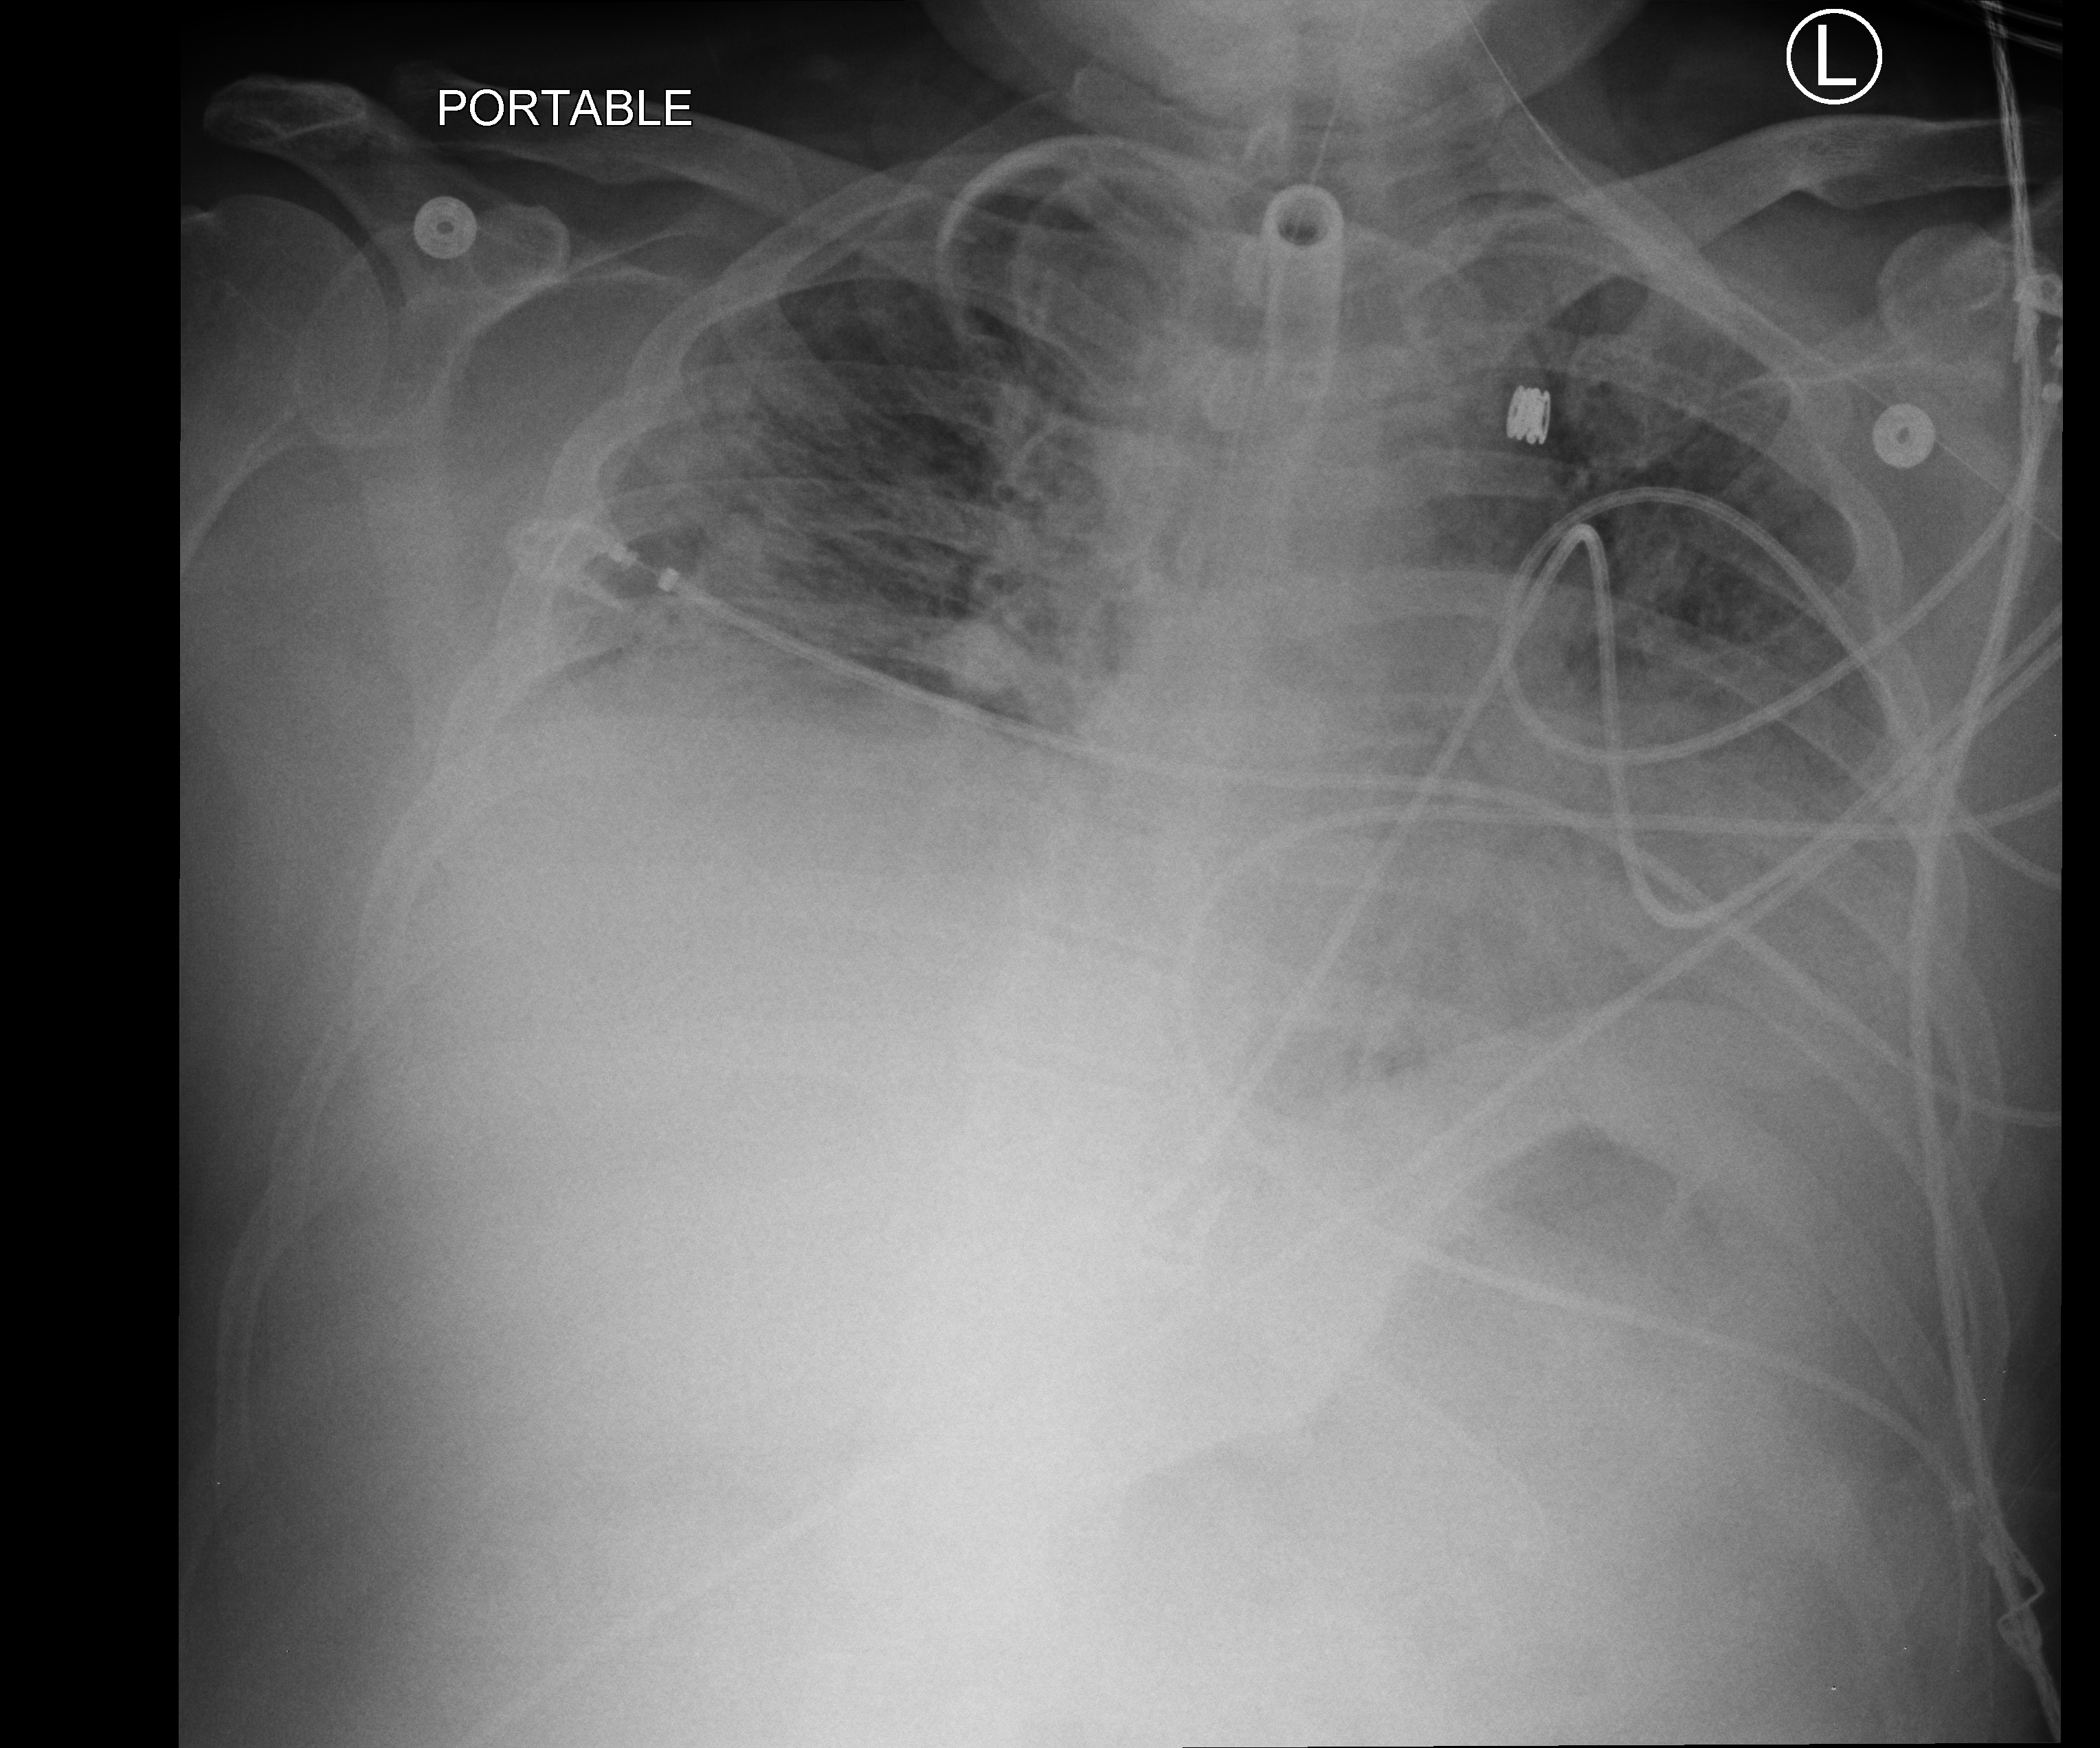
Portable chest radiograph; anteroposterior (AP) projection. Male patient hospitalised with COVID-19, age 18–59 years.
Hospital-stay facts (about this admission, not read from this image; timing relative to this image not recorded):
- mechanically ventilated during this hospital stay: yes
- length of hospital stay: 80 days
- admitted to intensive care during this hospital stay: yes